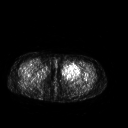
FDG PET of an extremity soft-tissue mass (from a PET/CT study), one axial slice; 3.27 mm slice thickness; 128 × 128 image matrix, field of view 500 × 500 mm. Patient: female, 42 years. Case-level facts recorded for this patient, not image findings: histological type: pleiomorphic leiomyosarcoma; grade: intermediate; site of the primary tumour: left thigh.
Annotated regions visible in this slice (expert contour drawn on MRI and transferred to this co-registered scan by the dataset authors):
- gross tumour volume including surrounding oedema: bounding box <61,63,81,80> (left, top, right, bottom; pixels)
- gross tumour volume (mass): <61,63,81,80>